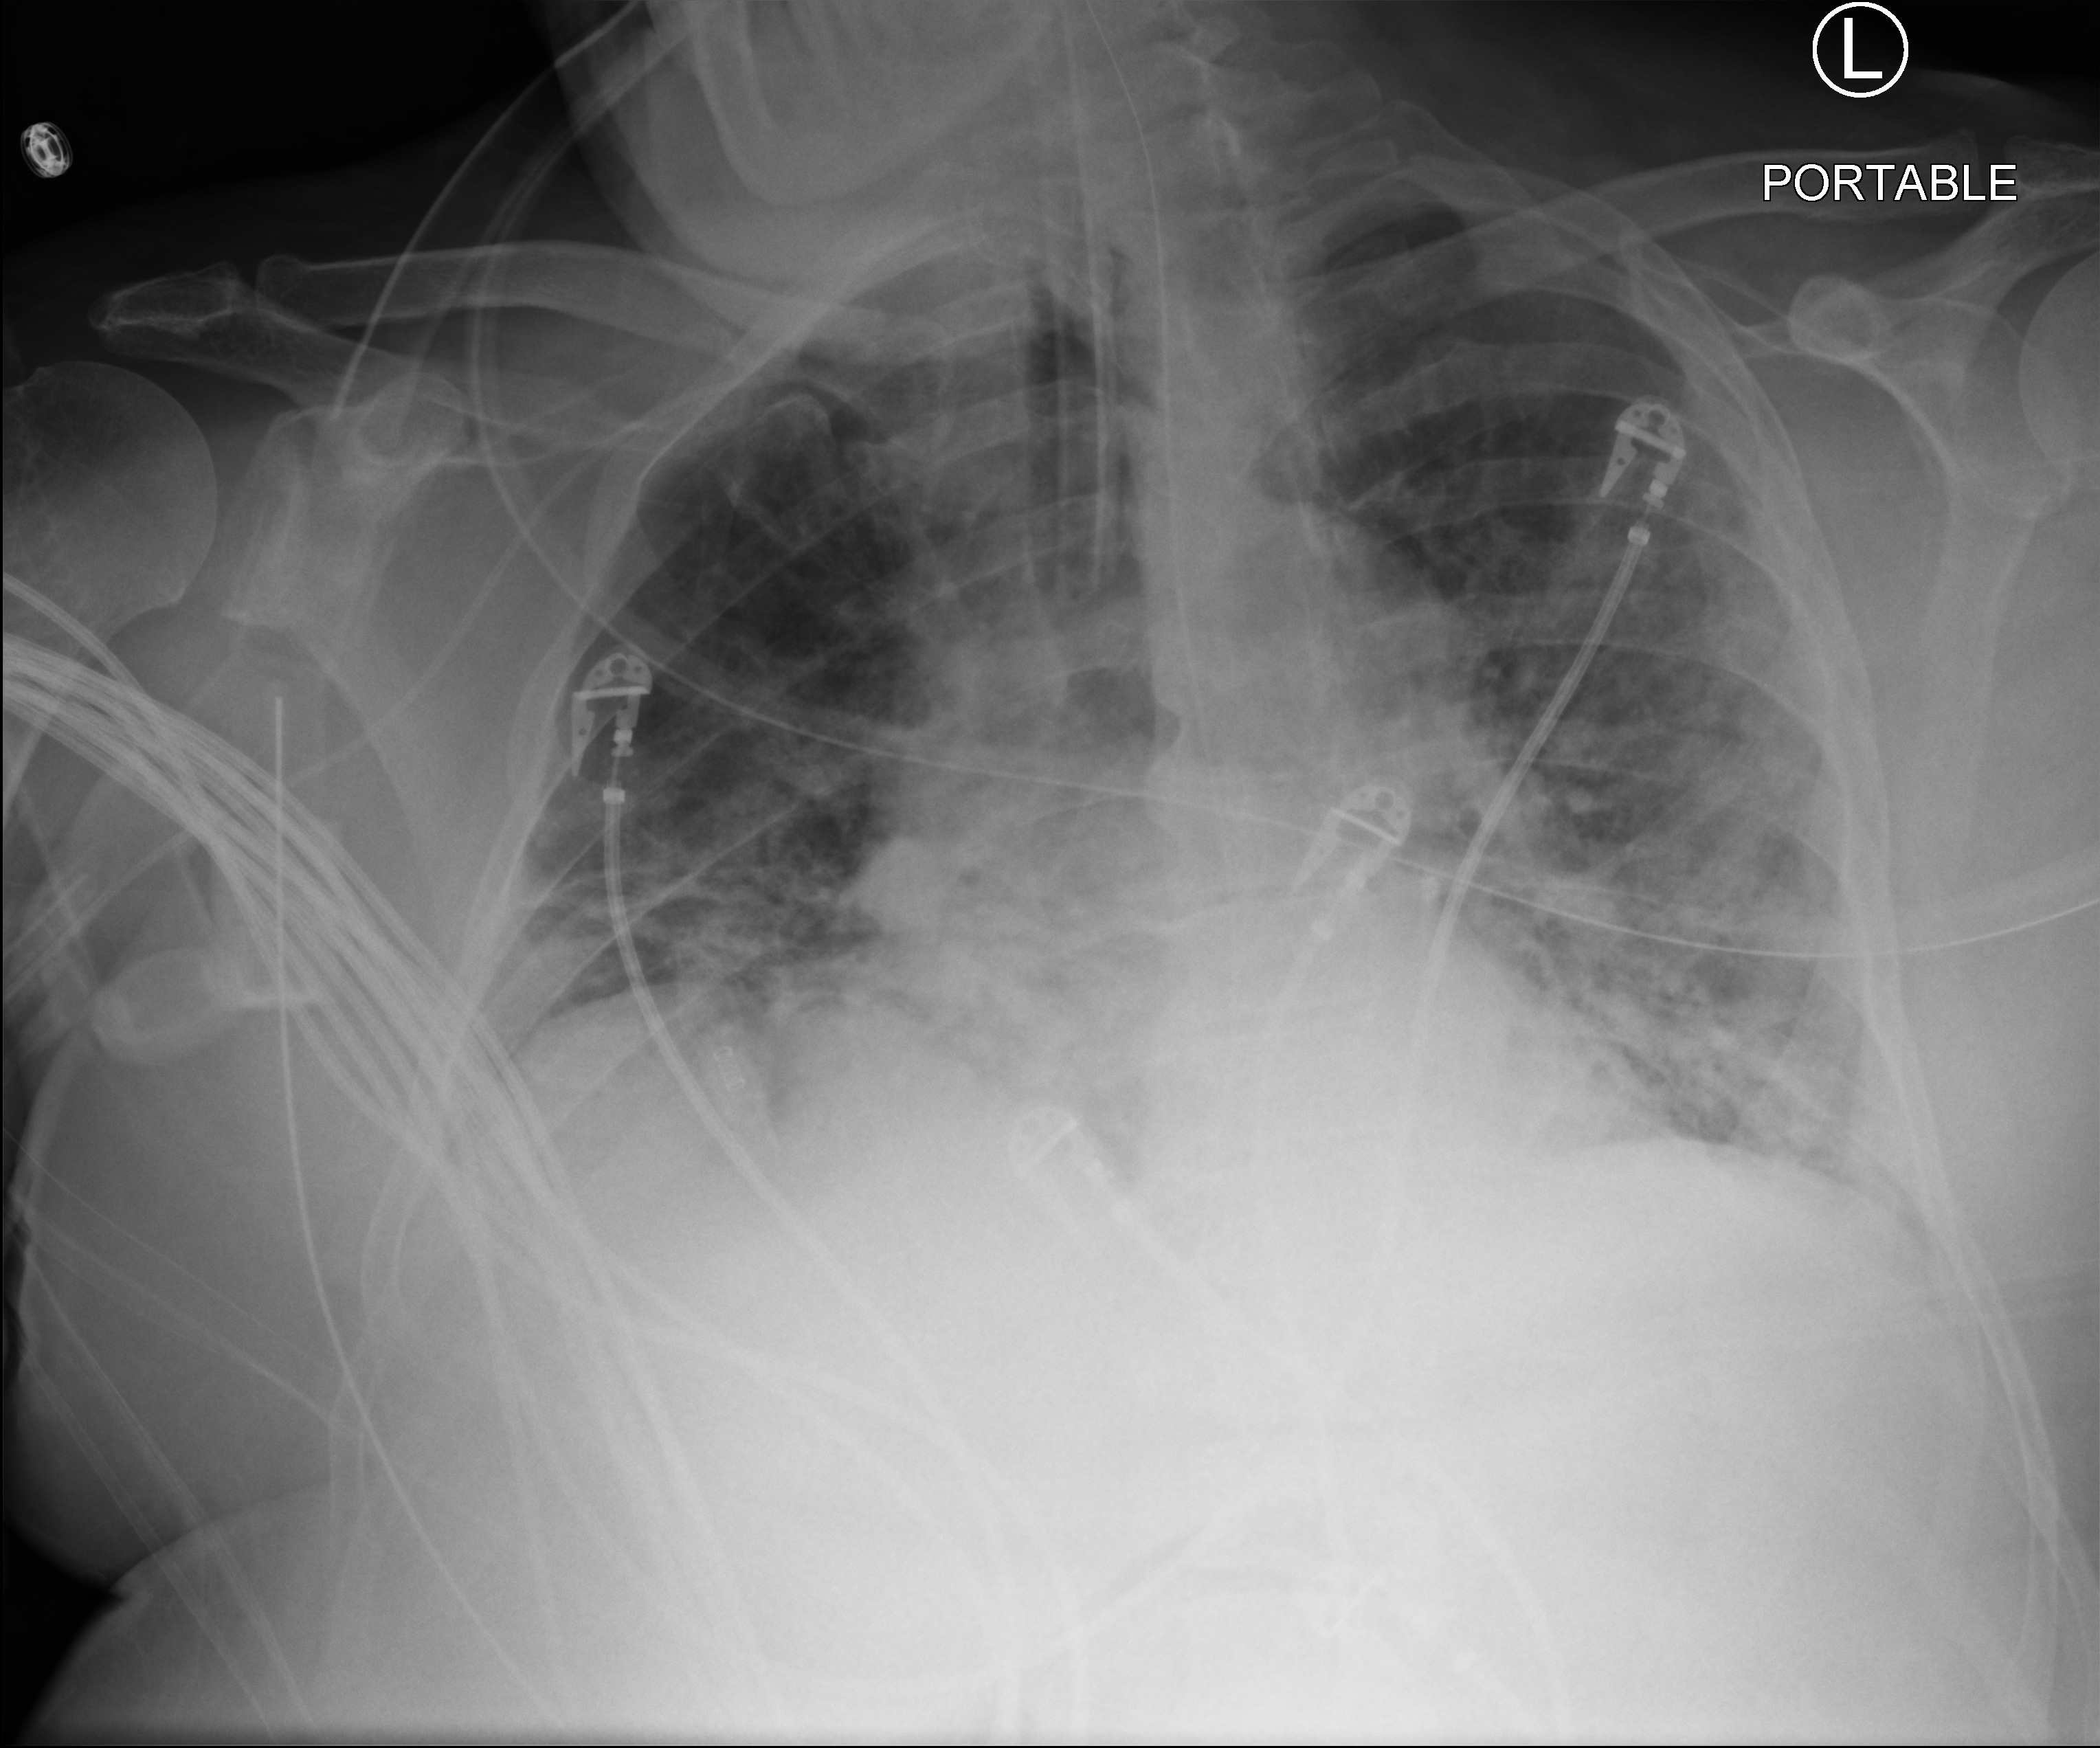
Chest X-ray (portable), anteroposterior (AP) projection. Male patient hospitalised with COVID-19, age 60–74 years.
Admission-level facts for this patient (not findings on this image; timing relative to this image not recorded):
- mechanically ventilated during this hospital stay: yes
- smoking status (admission record): never
- admitted to intensive care during this hospital stay: yes